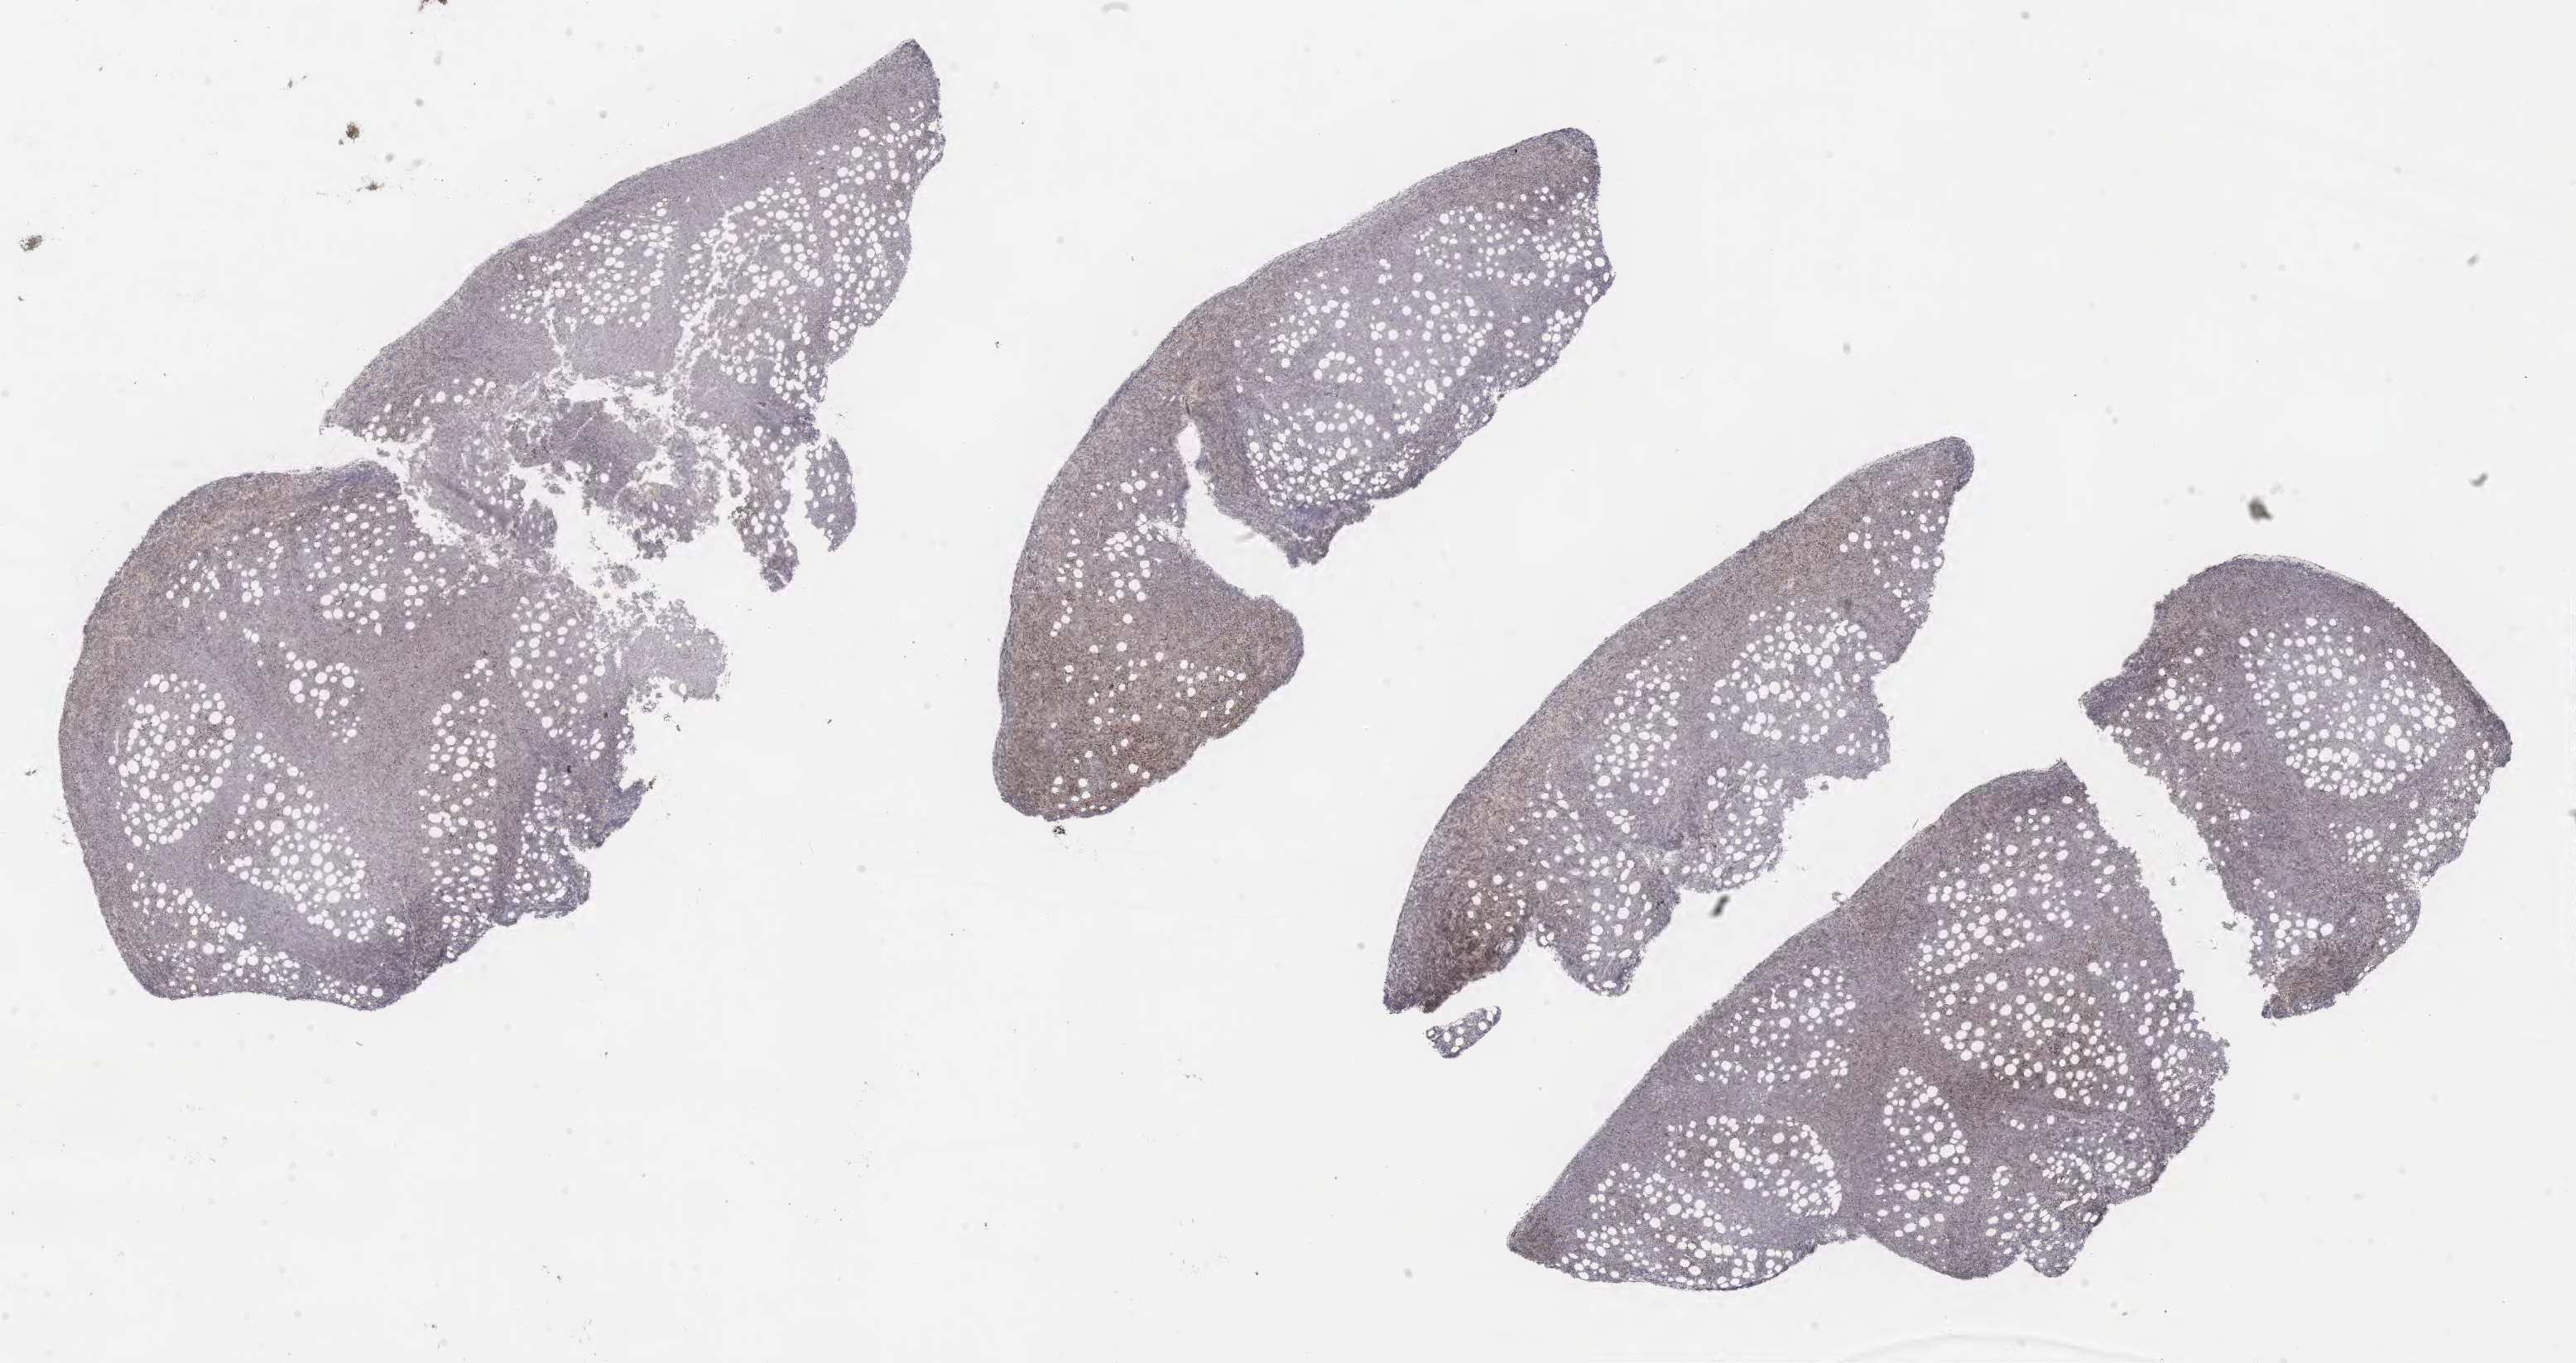
Immunohistochemistry (IHC) whole-slide image stained for BCL6 — shown as a low-resolution overview of the whole scanned area (about 25.2 x 13.3 mm). Specimen: tumor tissue. Male patient, aged 52.
Diagnosis: Diffuse large B-cell lymphoma, NOS.